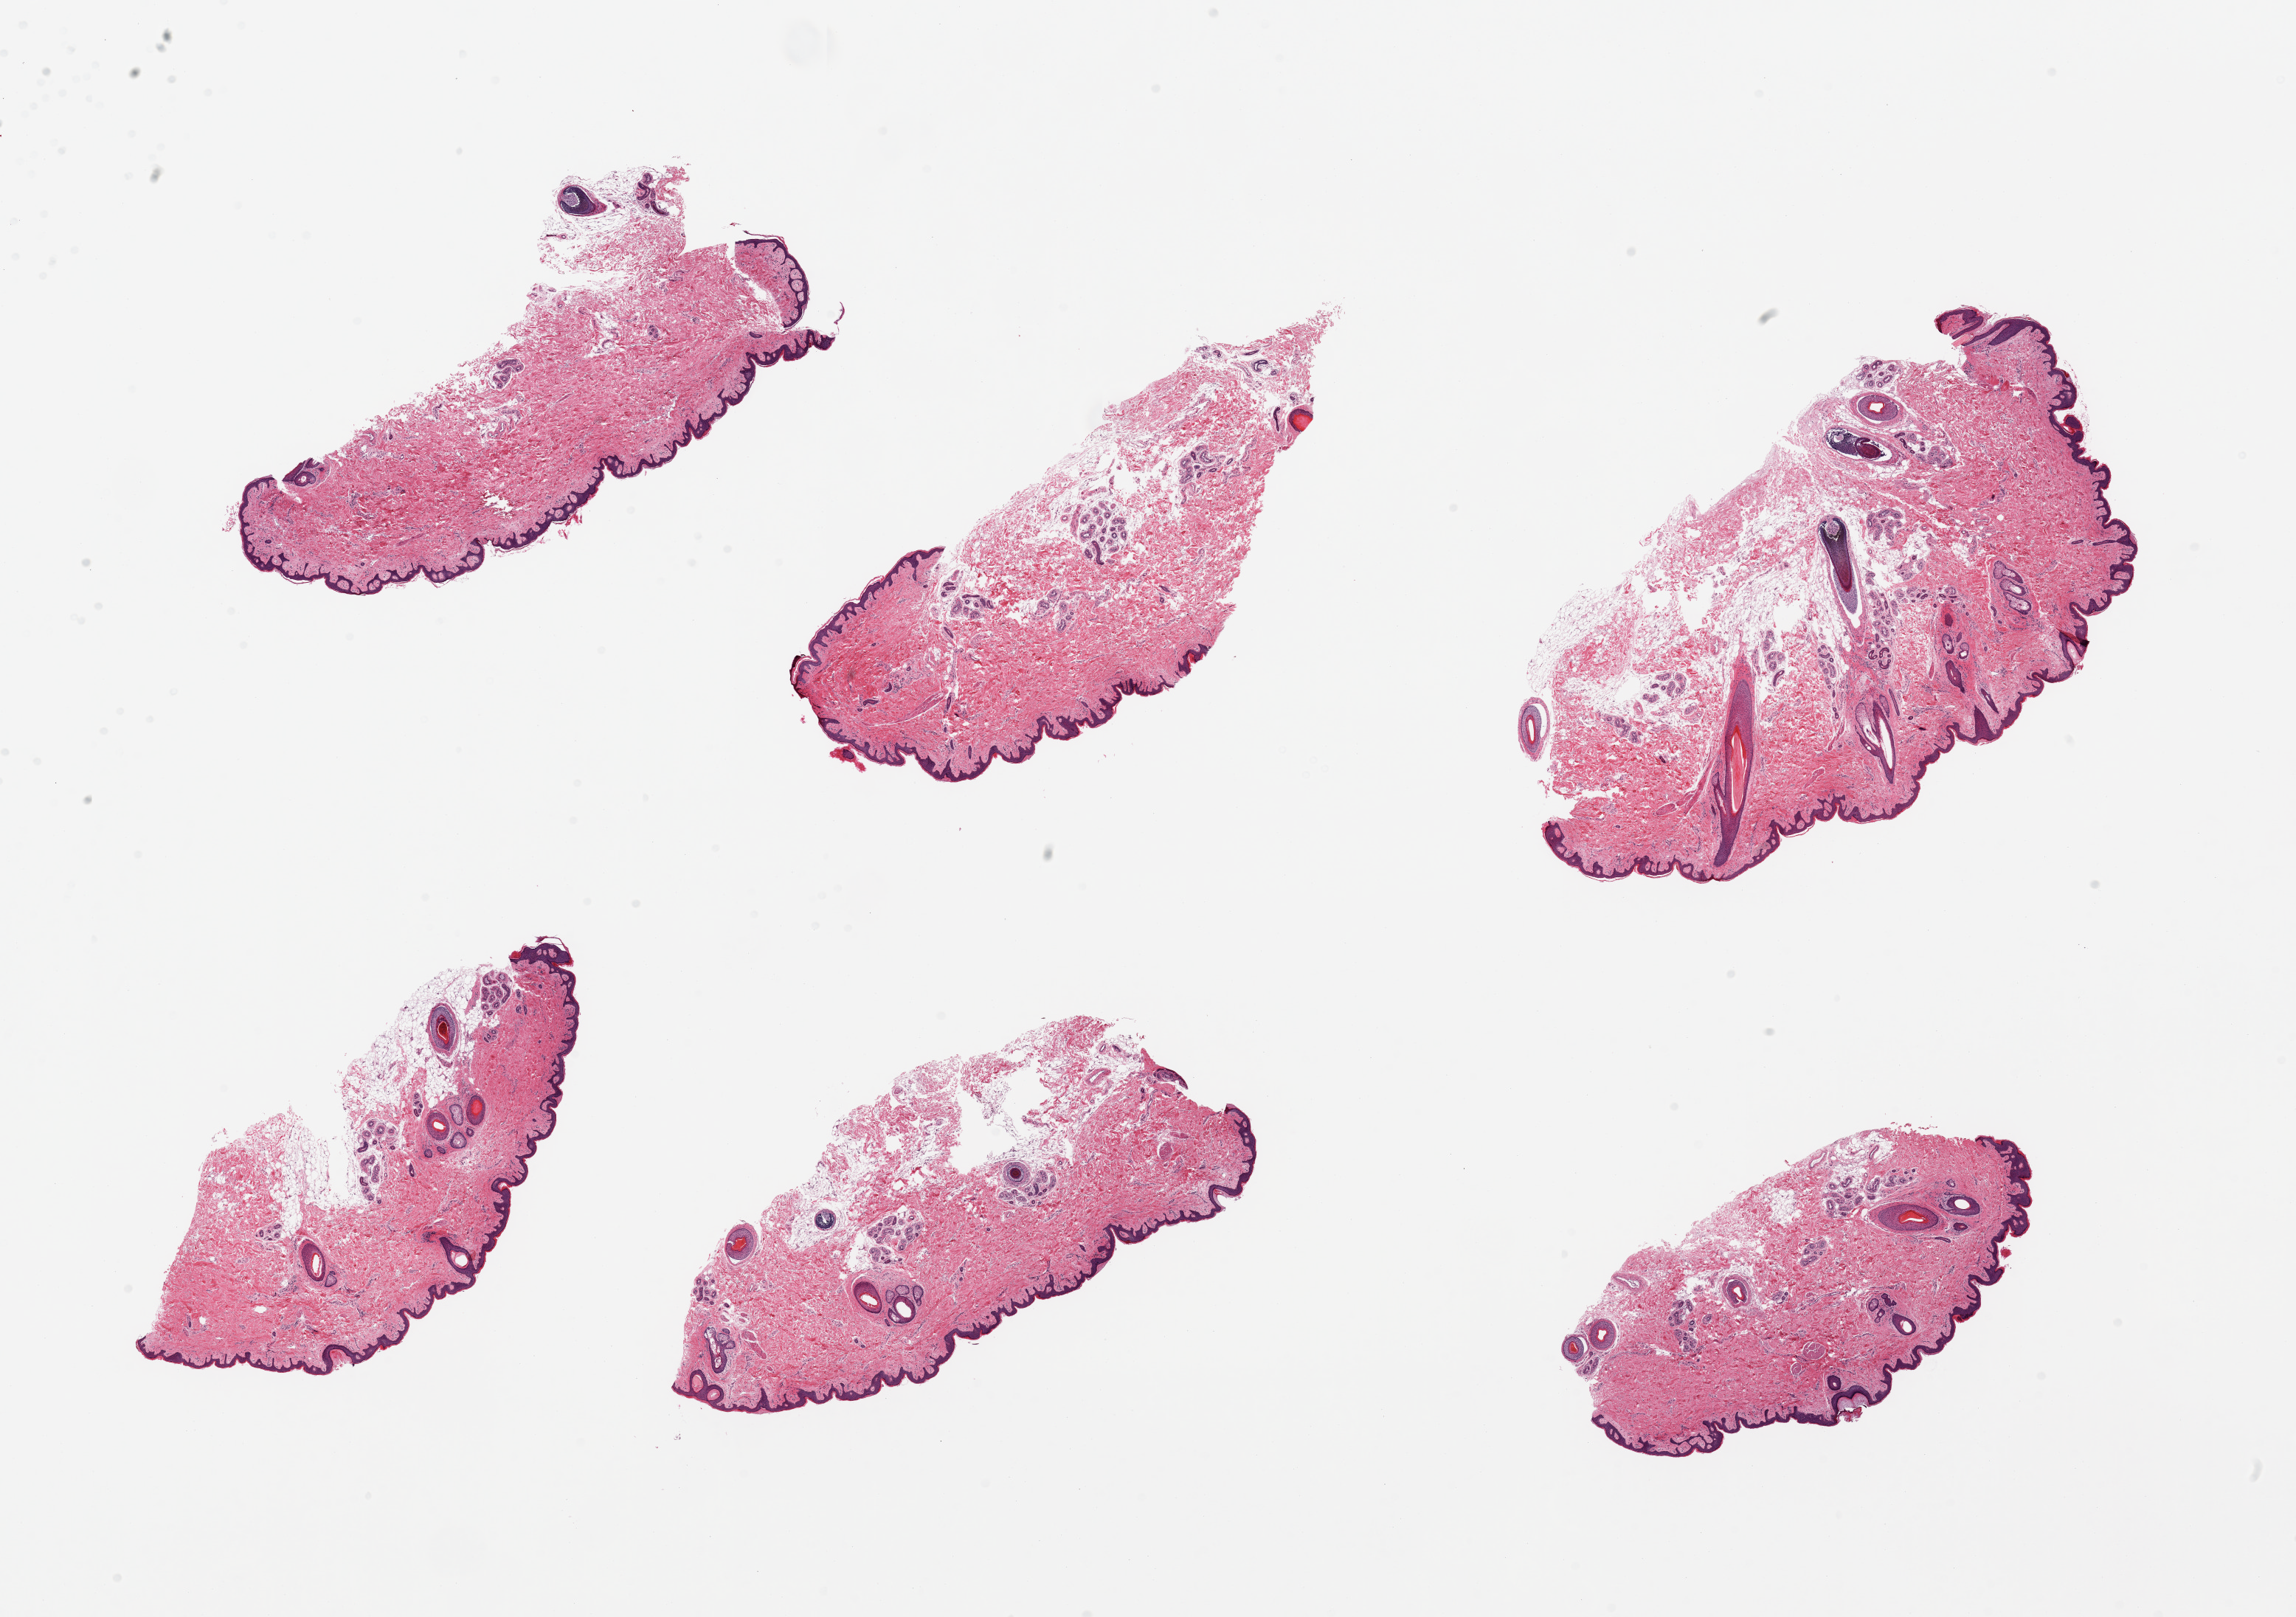
Whole-slide image, H&E stain, whole scanned area (about 24.6 x 17.3 mm, from a 20x scan) shown as a low-resolution overview, PAXgene-fixed paraffin-embedded (PFPE) section, sampled site (target tissue): skin of suprapubic region, donor tissue sample. Donor sex: male.
Review note (as recorded): 6 pieces; hair shaft density varies from 1 to 5 per piece.